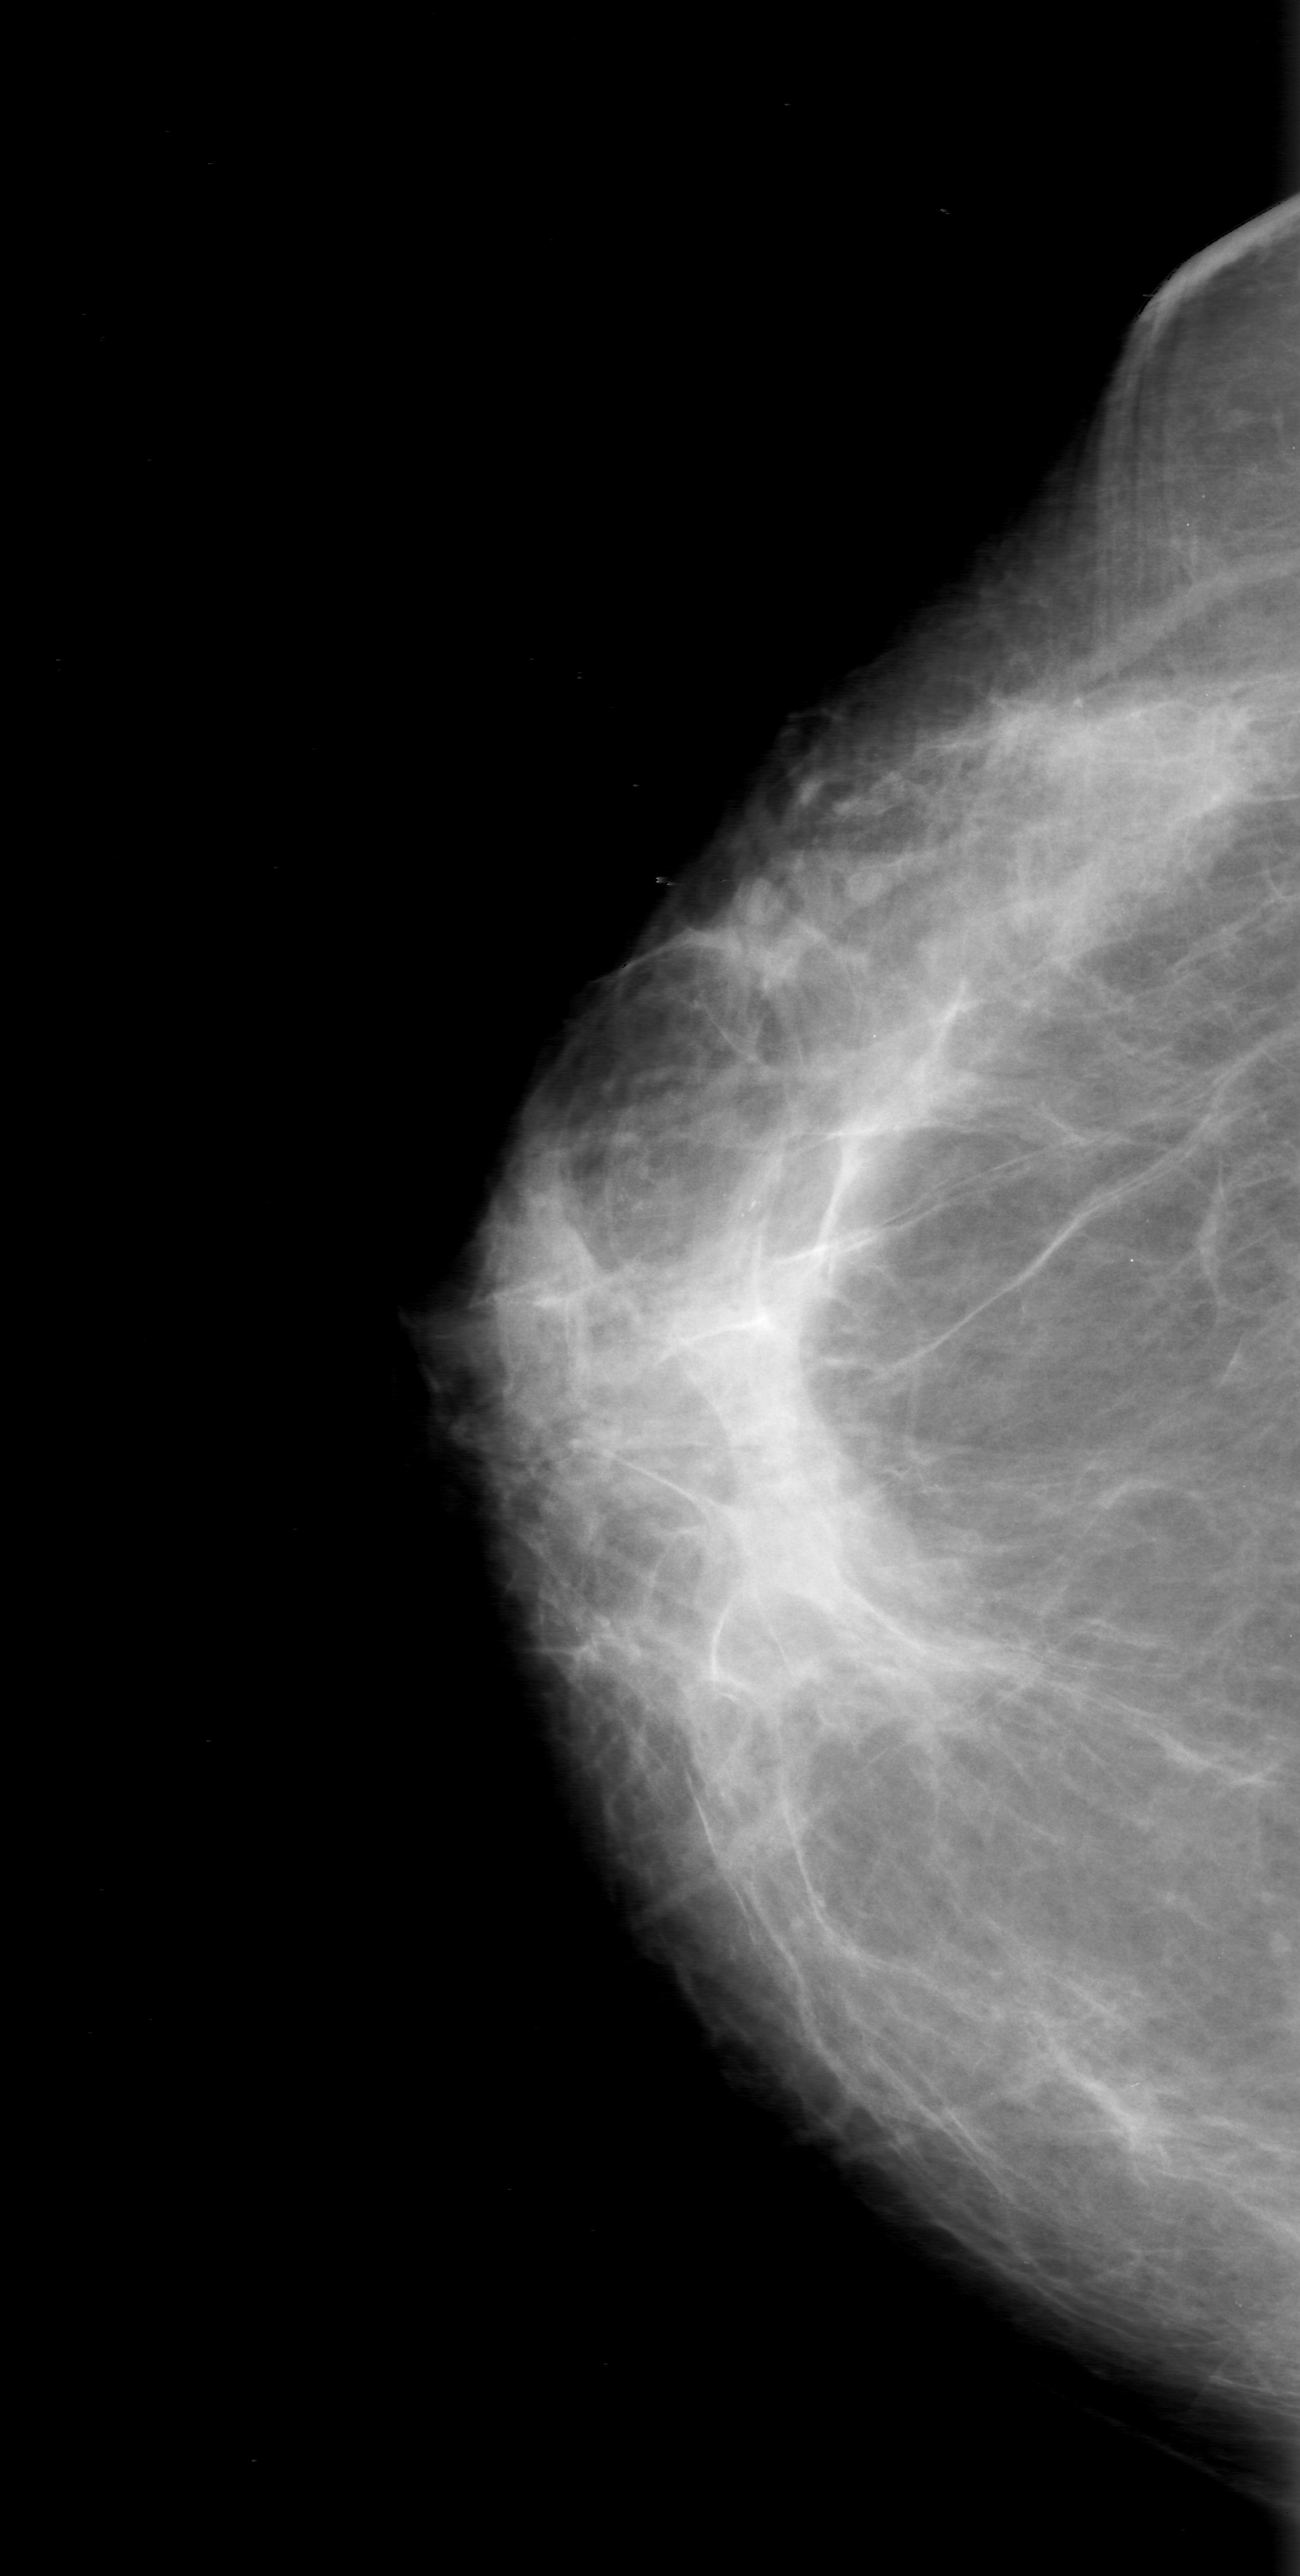
Mammogram (digitized film); right breast; CC view; BI-RADS breast density category 2 (scale 1–4); 1300 × 2576 image matrix.
Expert-marked regions of interest on this film, with their recorded descriptors:
- calcifications, morphology amorphous, distribution clustered; BI-RADS assessment category 0; pathology (as recorded): benign: bounding box <462,1101,819,1456> (left, top, right, bottom; pixels)